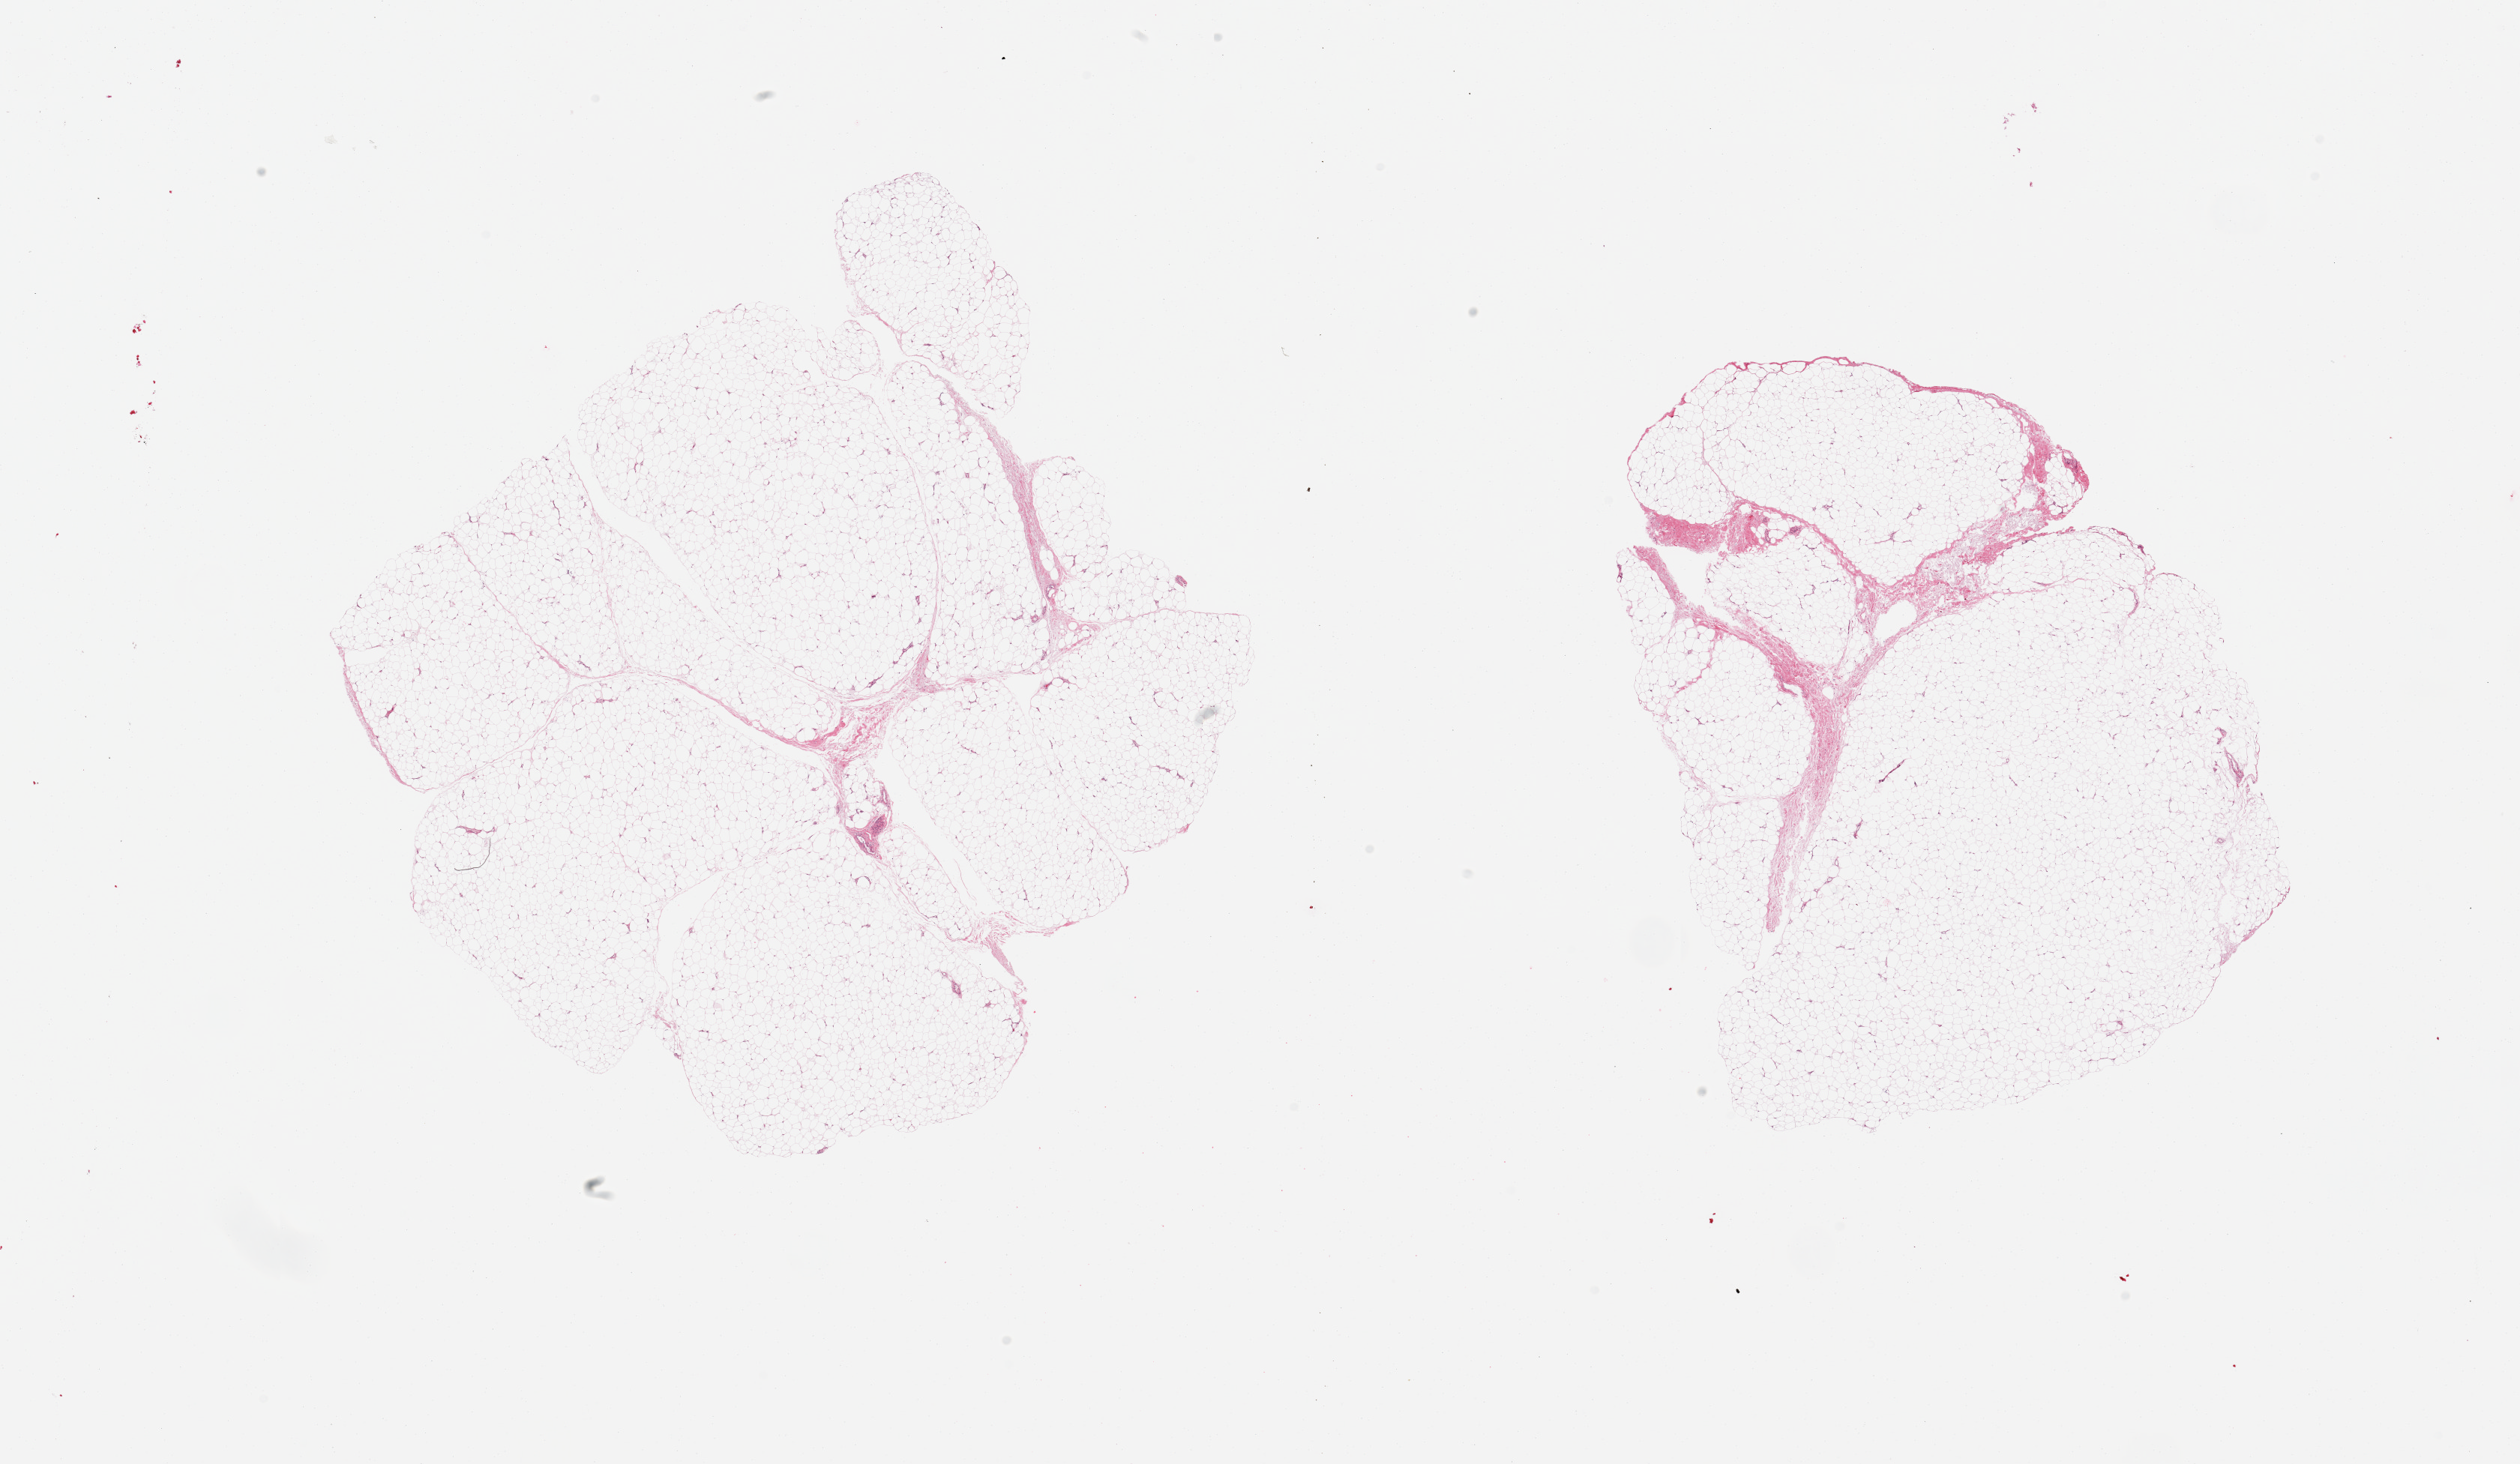
Digitized haematoxylin and eosin-stained section, brightfield — low-resolution overview of the scanned area, about 26.6 x 15.4 mm, PAXgene-fixed, paraffin-embedded tissue, sampled site (target tissue): adipose tissue, tissue donor sample.
Review note (as recorded): 2 pieces, fascia up to ~10% of specimen.